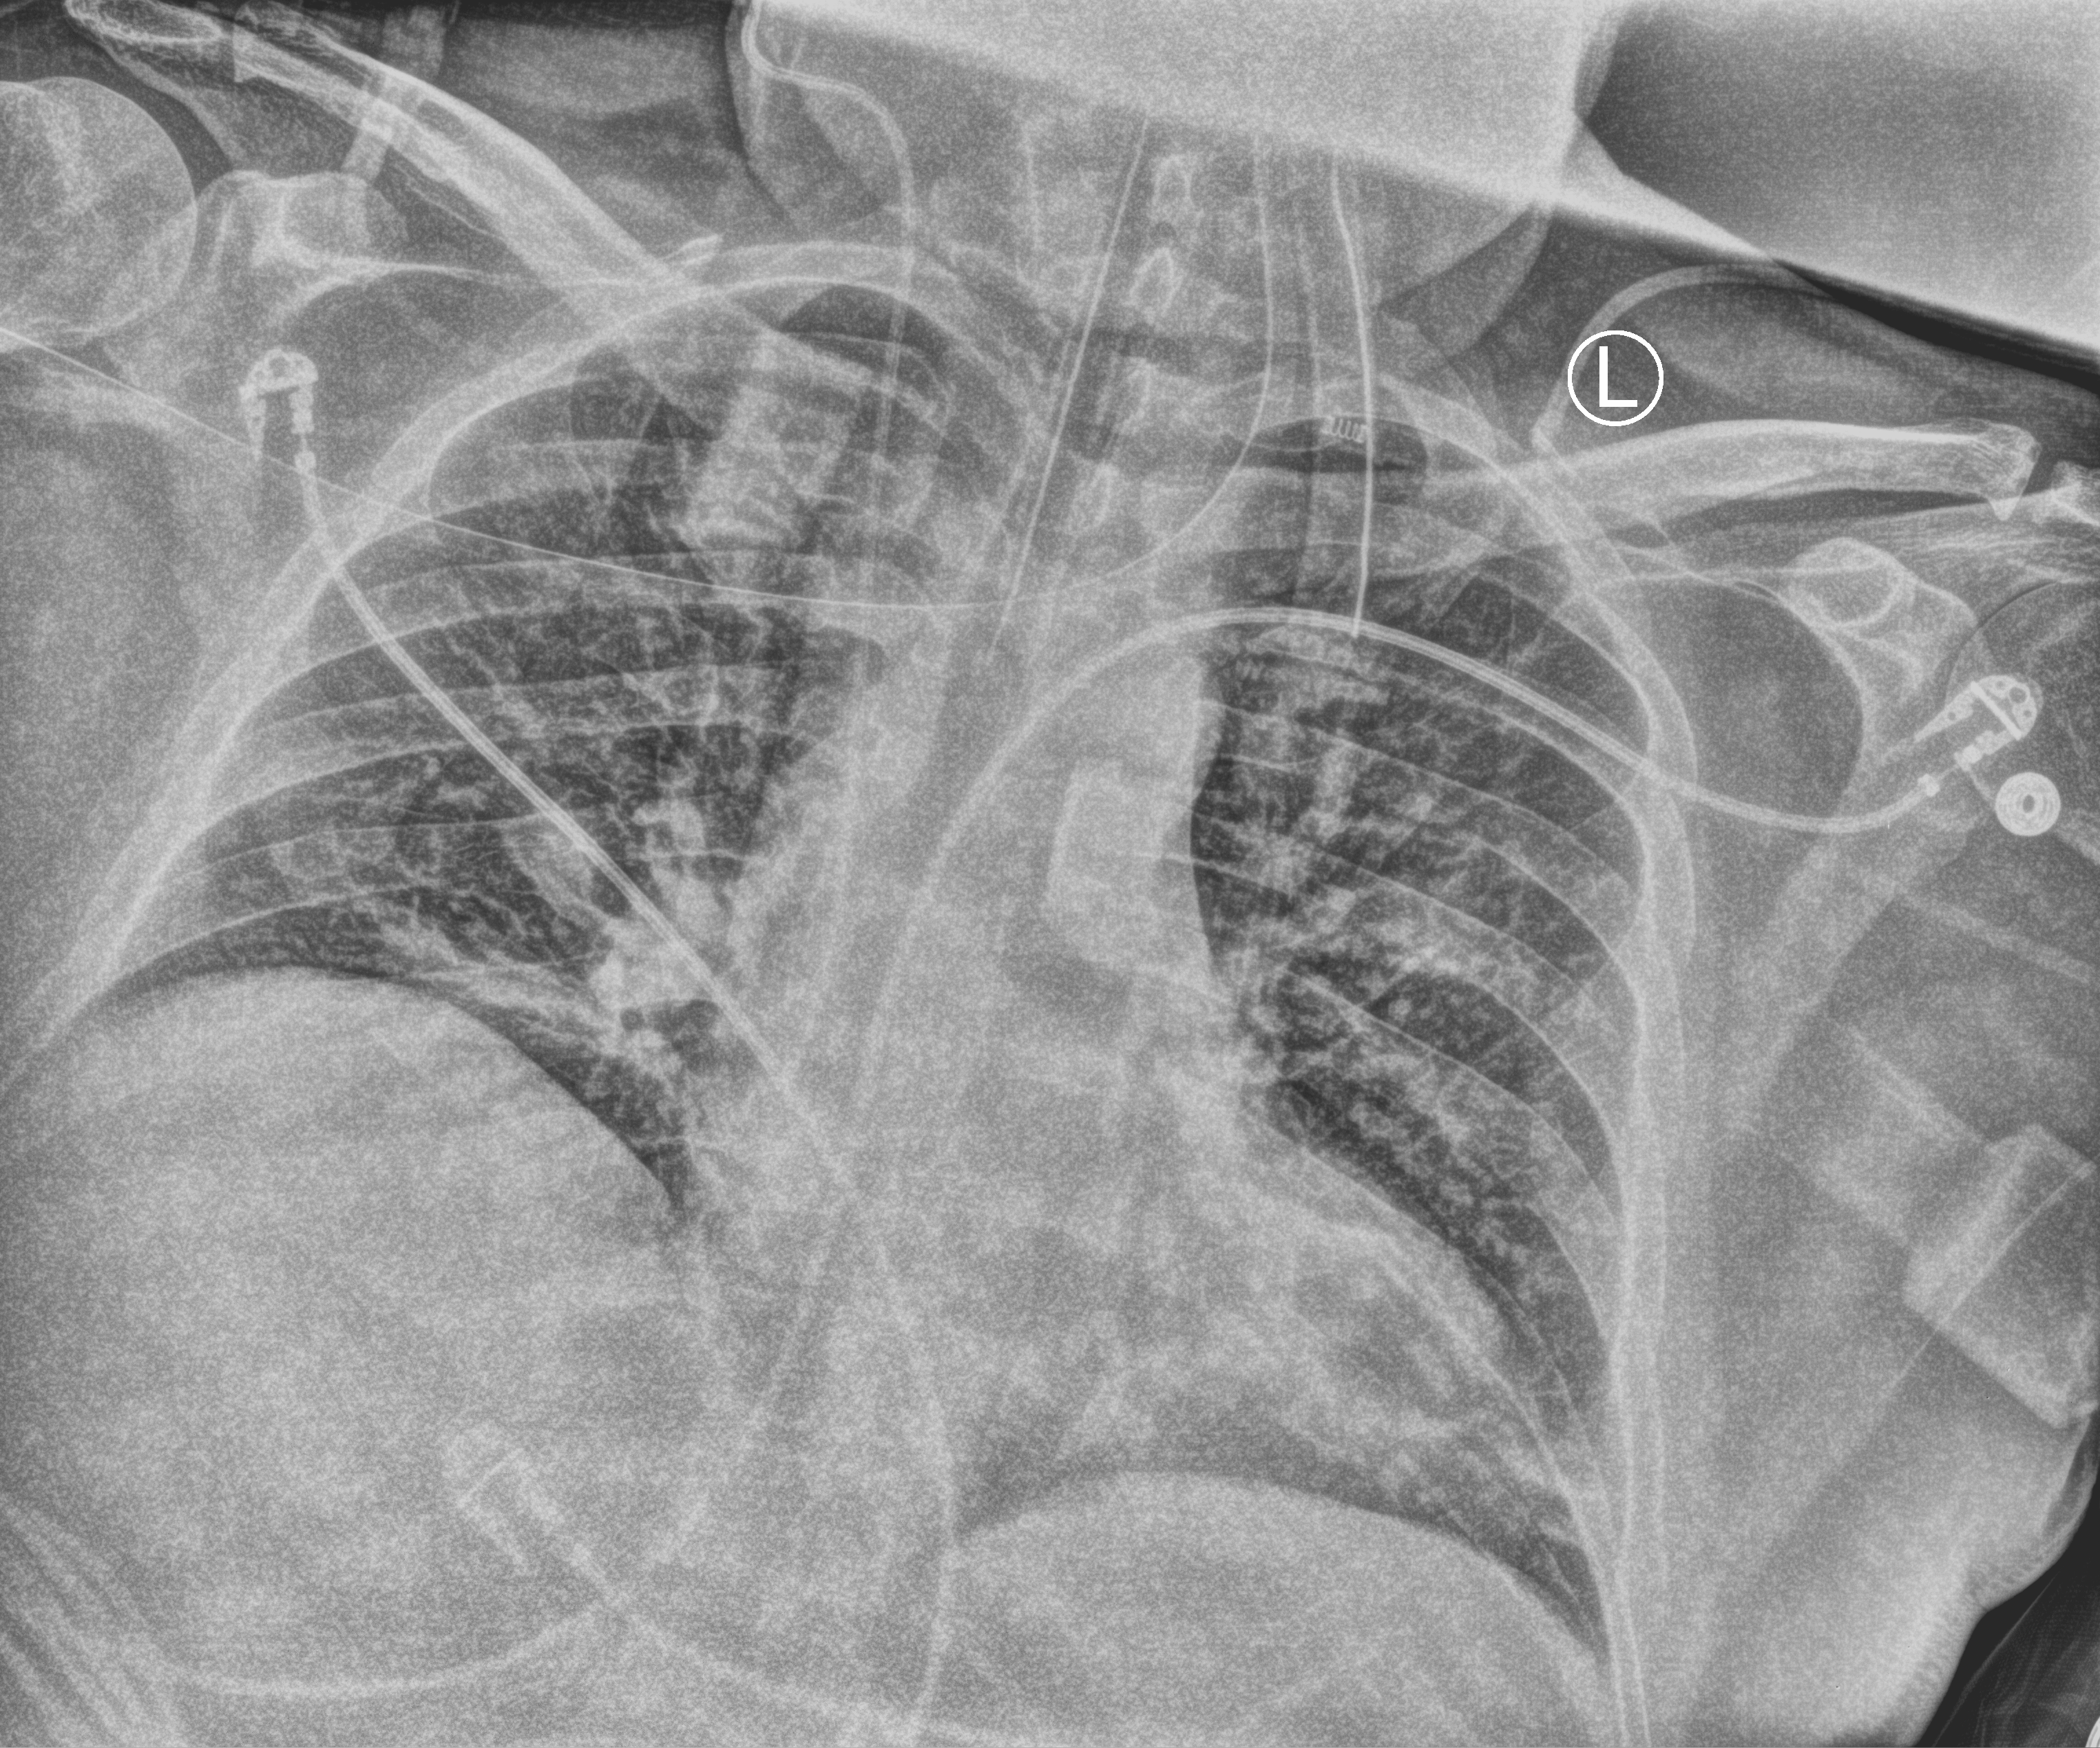
Portable chest radiograph, anteroposterior (AP) projection. Male patient hospitalised with COVID-19, age 18–59 years.
Hospital-stay facts (about this admission, not read from this image; timing relative to this image not recorded): mechanically ventilated during this hospital stay: yes.